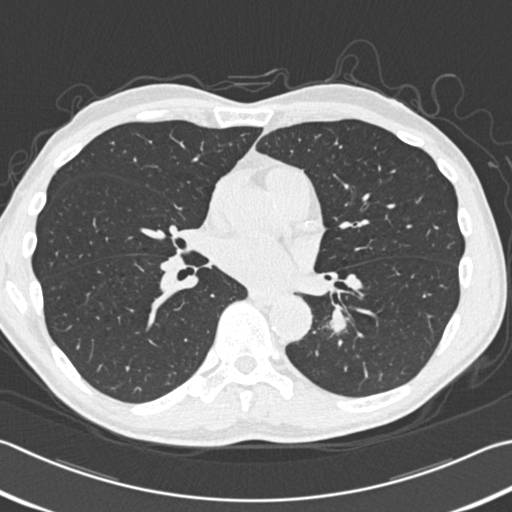
Low-dose screening chest CT, one axial slice. Position 172 of 354 along the scan axis. 120 kVp. Lung window (W 1500 / L -600 HU). 512 × 512 image matrix, field of view 346 × 346 mm.
Annotated regions visible in this slice (manually delineated by an expert):
- lesion 1 (tumor, lower lobe of left lung): bounding box [x1, y1, x2, y2] px = [330, 312, 346, 334]